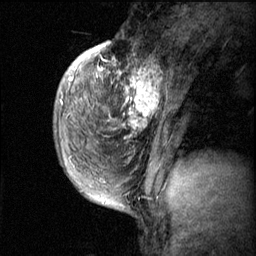
Breast MRI (dynamic contrast-enhanced), one sagittal slice. Slice 16 of 60 in the series (ordered by position). Dynamic contrast-enhanced series, image 2 of 3 at this slice position (ordered by acquisition). 1.5 T. TE 4.2 ms, TR 11.1 ms. 256 × 256 image matrix. Female patient, age 50 years.
Structures marked on this image (semi-automatically segmented with operator editing):
- analysis volume of interest (the breast-tissue region the enhancement analysis was run in; not a lesion): bounding box (x1, y1, x2, y2) in pixels: (82, 56, 168, 143)
- tumour enhancement mask (voxels above the 70 % enhancement threshold inside the analysis volume of interest): (85, 56, 160, 131)